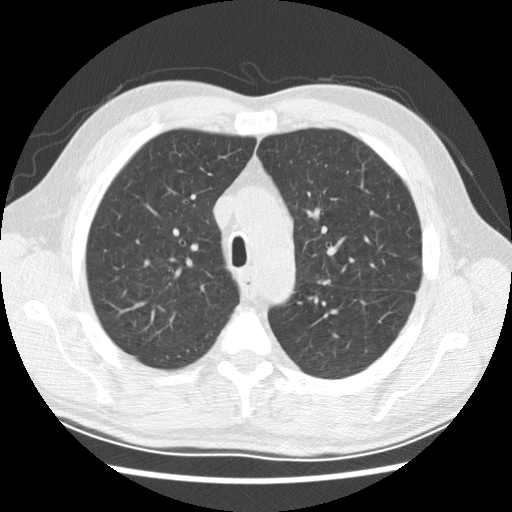
Axial slice from a low-dose chest CT screening exam, baseline annual screen, lung window (W 1500 / L -600 HU), 120 kVp, 512 × 512 image matrix, field of view 340 × 340 mm. Male participant, aged 59 years at enrolment.
Expert-annotated lung lesion, box from (x=301, y=269) to (x=342, y=295) px. The exam's reader record, not a measurement of the box and not confirmed to be the same lesion: non-calcified nodule or mass ≥4 mm, left upper lobe, 8 × 5 mm, smooth margins, soft tissue attenuation. Official screen result: positive, change unspecified: nodule(s) >= 4 mm or enlarging nodule(s), mass(es), or other non-specific abnormalities suspicious for lung cancer. Later outcome: lung cancer diagnosed 645 days after this screen (after the second annual screen) — adenocarcinoma, NOS, left upper lobe, left lower lobe, poorly differentiated (G3), stage IV (AJCC 6th edition).